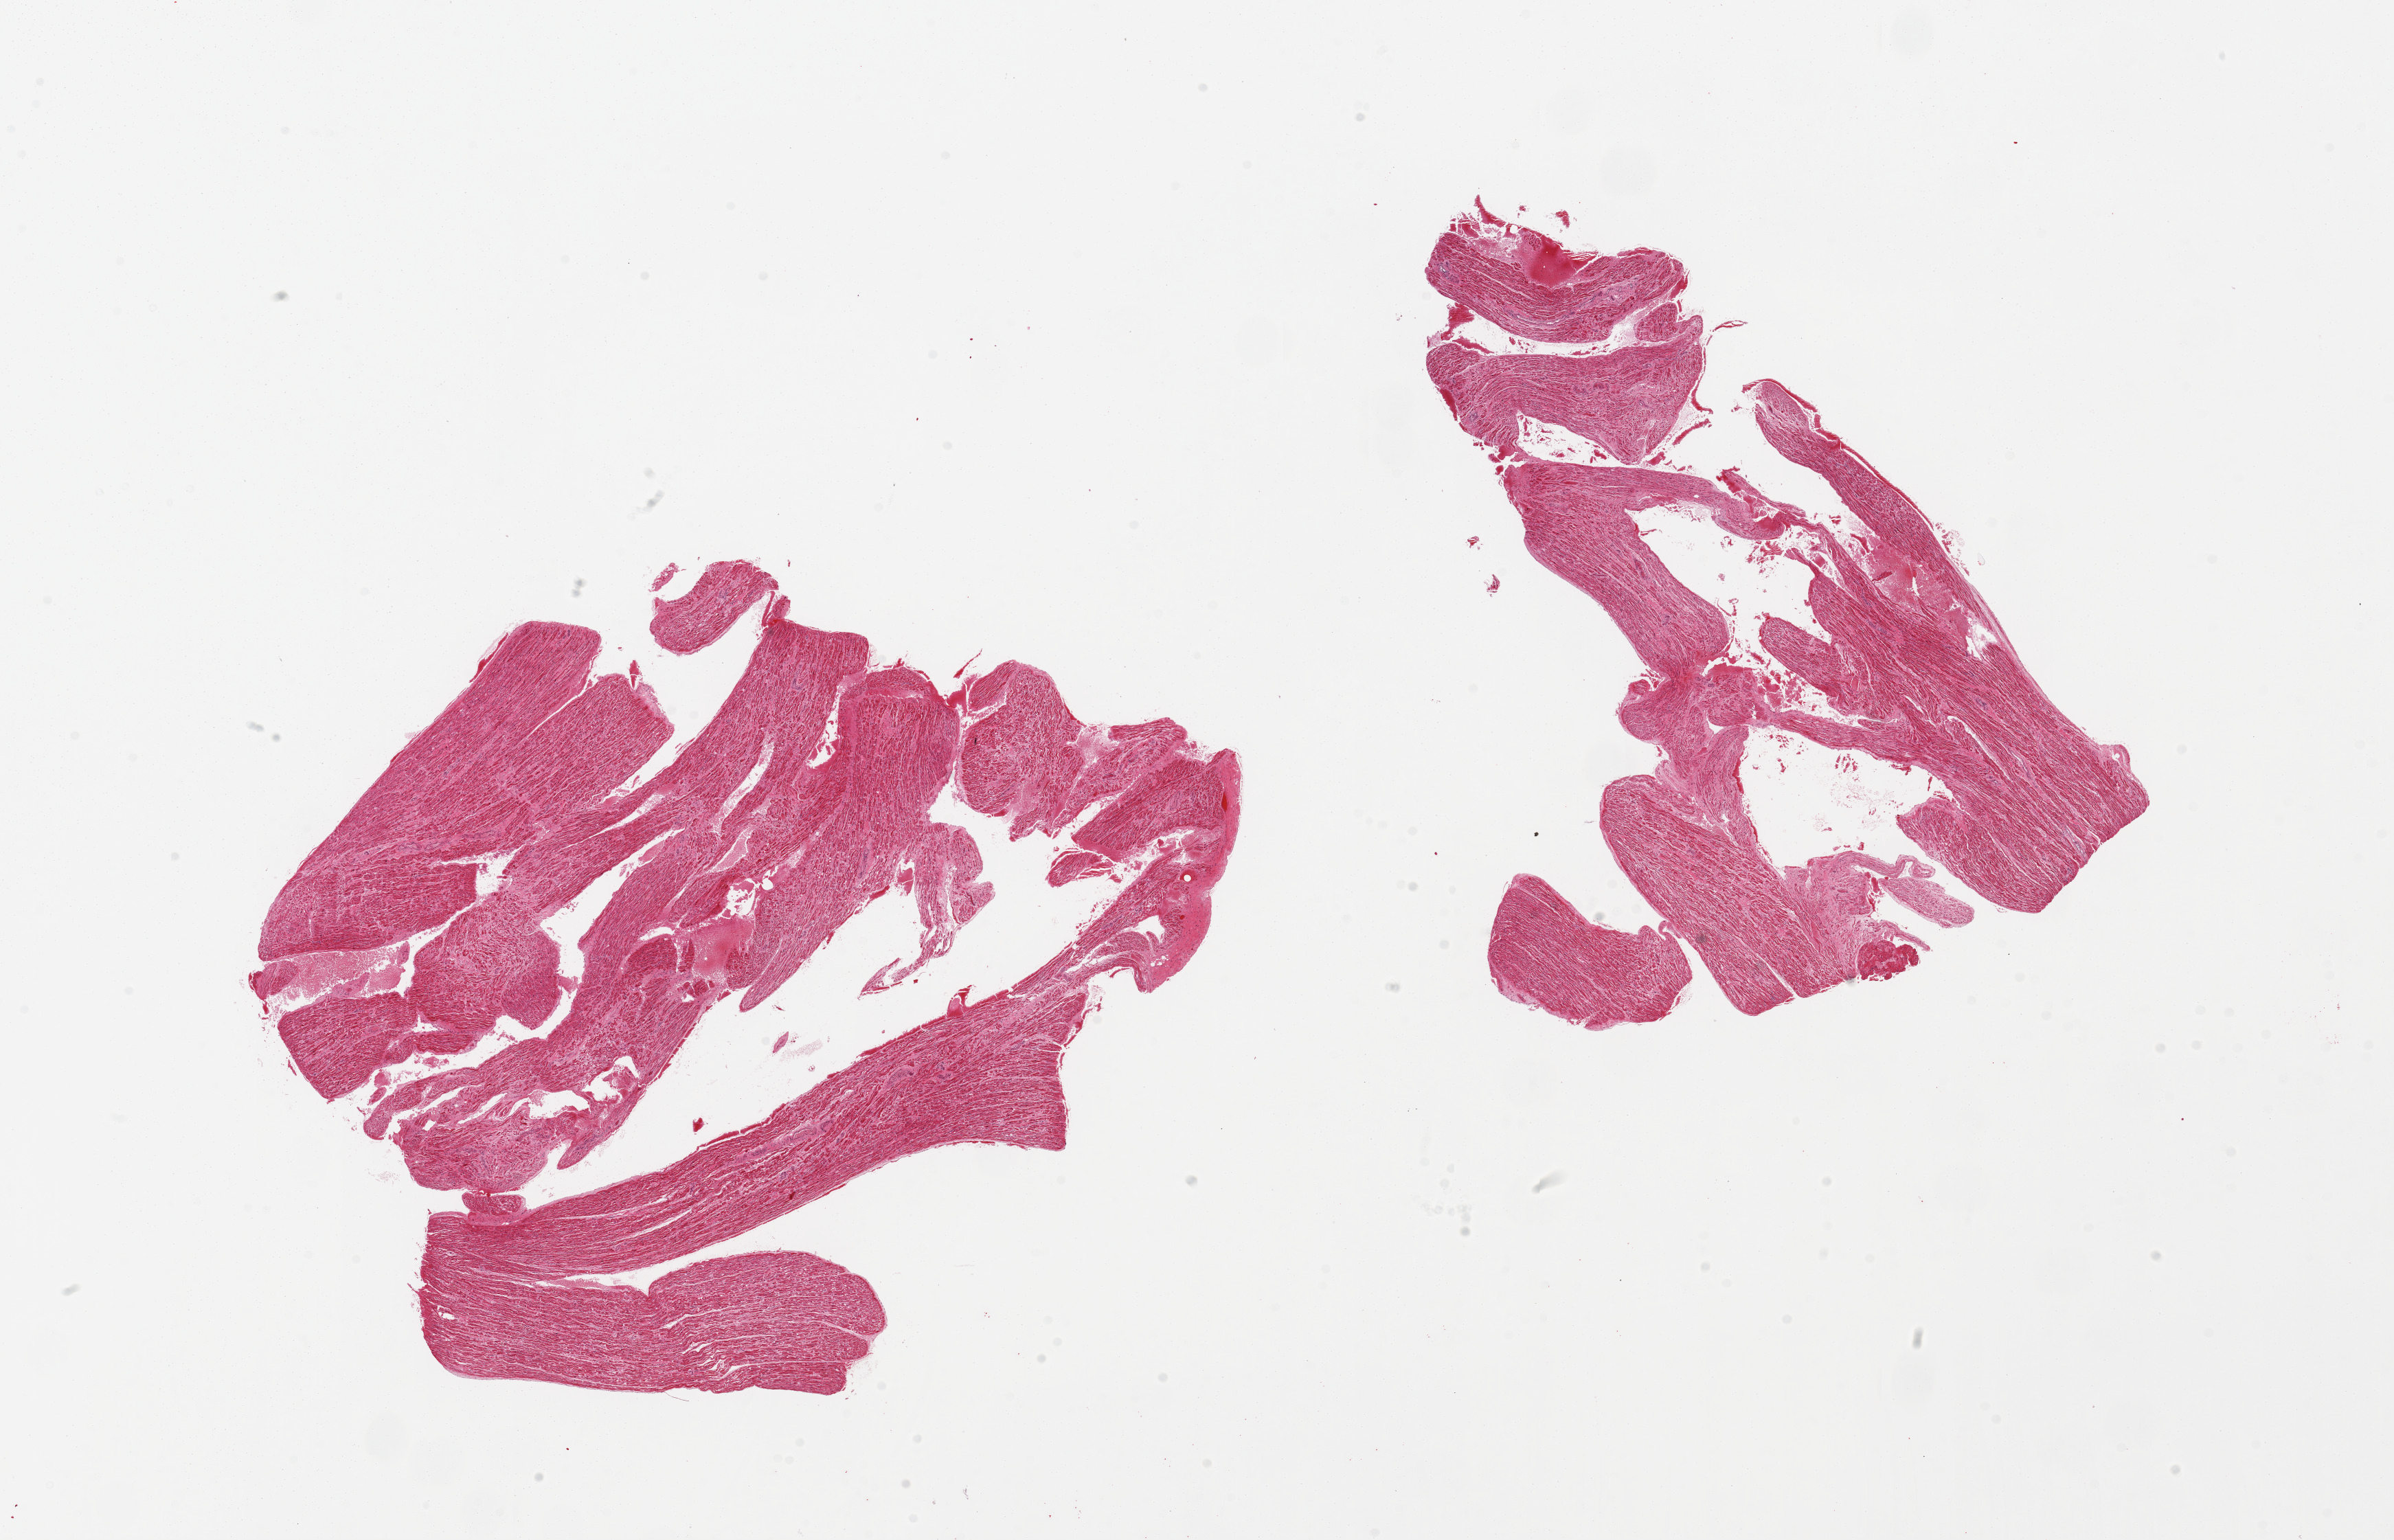
Digitized H&E-stained section, brightfield, a low-resolution overview of the entire scanned area, about 27.6 x 17.7 mm (slide scanned at 20x); PAXgene-fixed, paraffin-embedded tissue; section of auricular appendage (target tissue); tissue donor sample. Donor sex: male.
Pathologist's review note for this sample: 2 pieces.